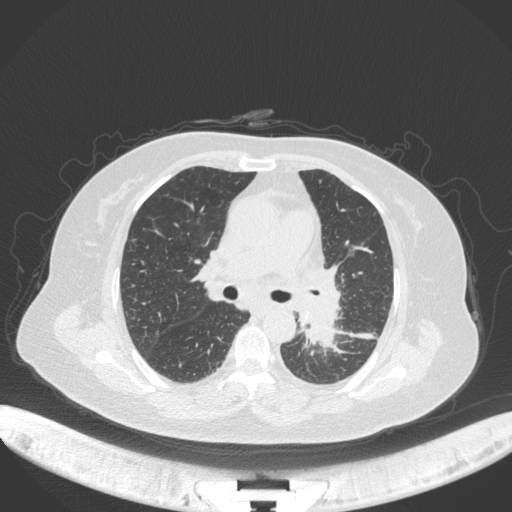
Chest CT, one axial slice. Position 207 of 328 along the scan axis. 120 kVp. Lung window (W 1500 / L -600 HU). 1 mm slice thickness. 512 × 512 image matrix. Patient: female, 69 years. From the clinical record (not read from this slice): clinical TNM (as recorded): T2b N3 M1.
Annotated regions visible in this slice (bounding box drawn by a radiologist):
- lung tumour (recorded histology: adenocarcinoma): box from (x=302, y=308) to (x=342, y=353) px